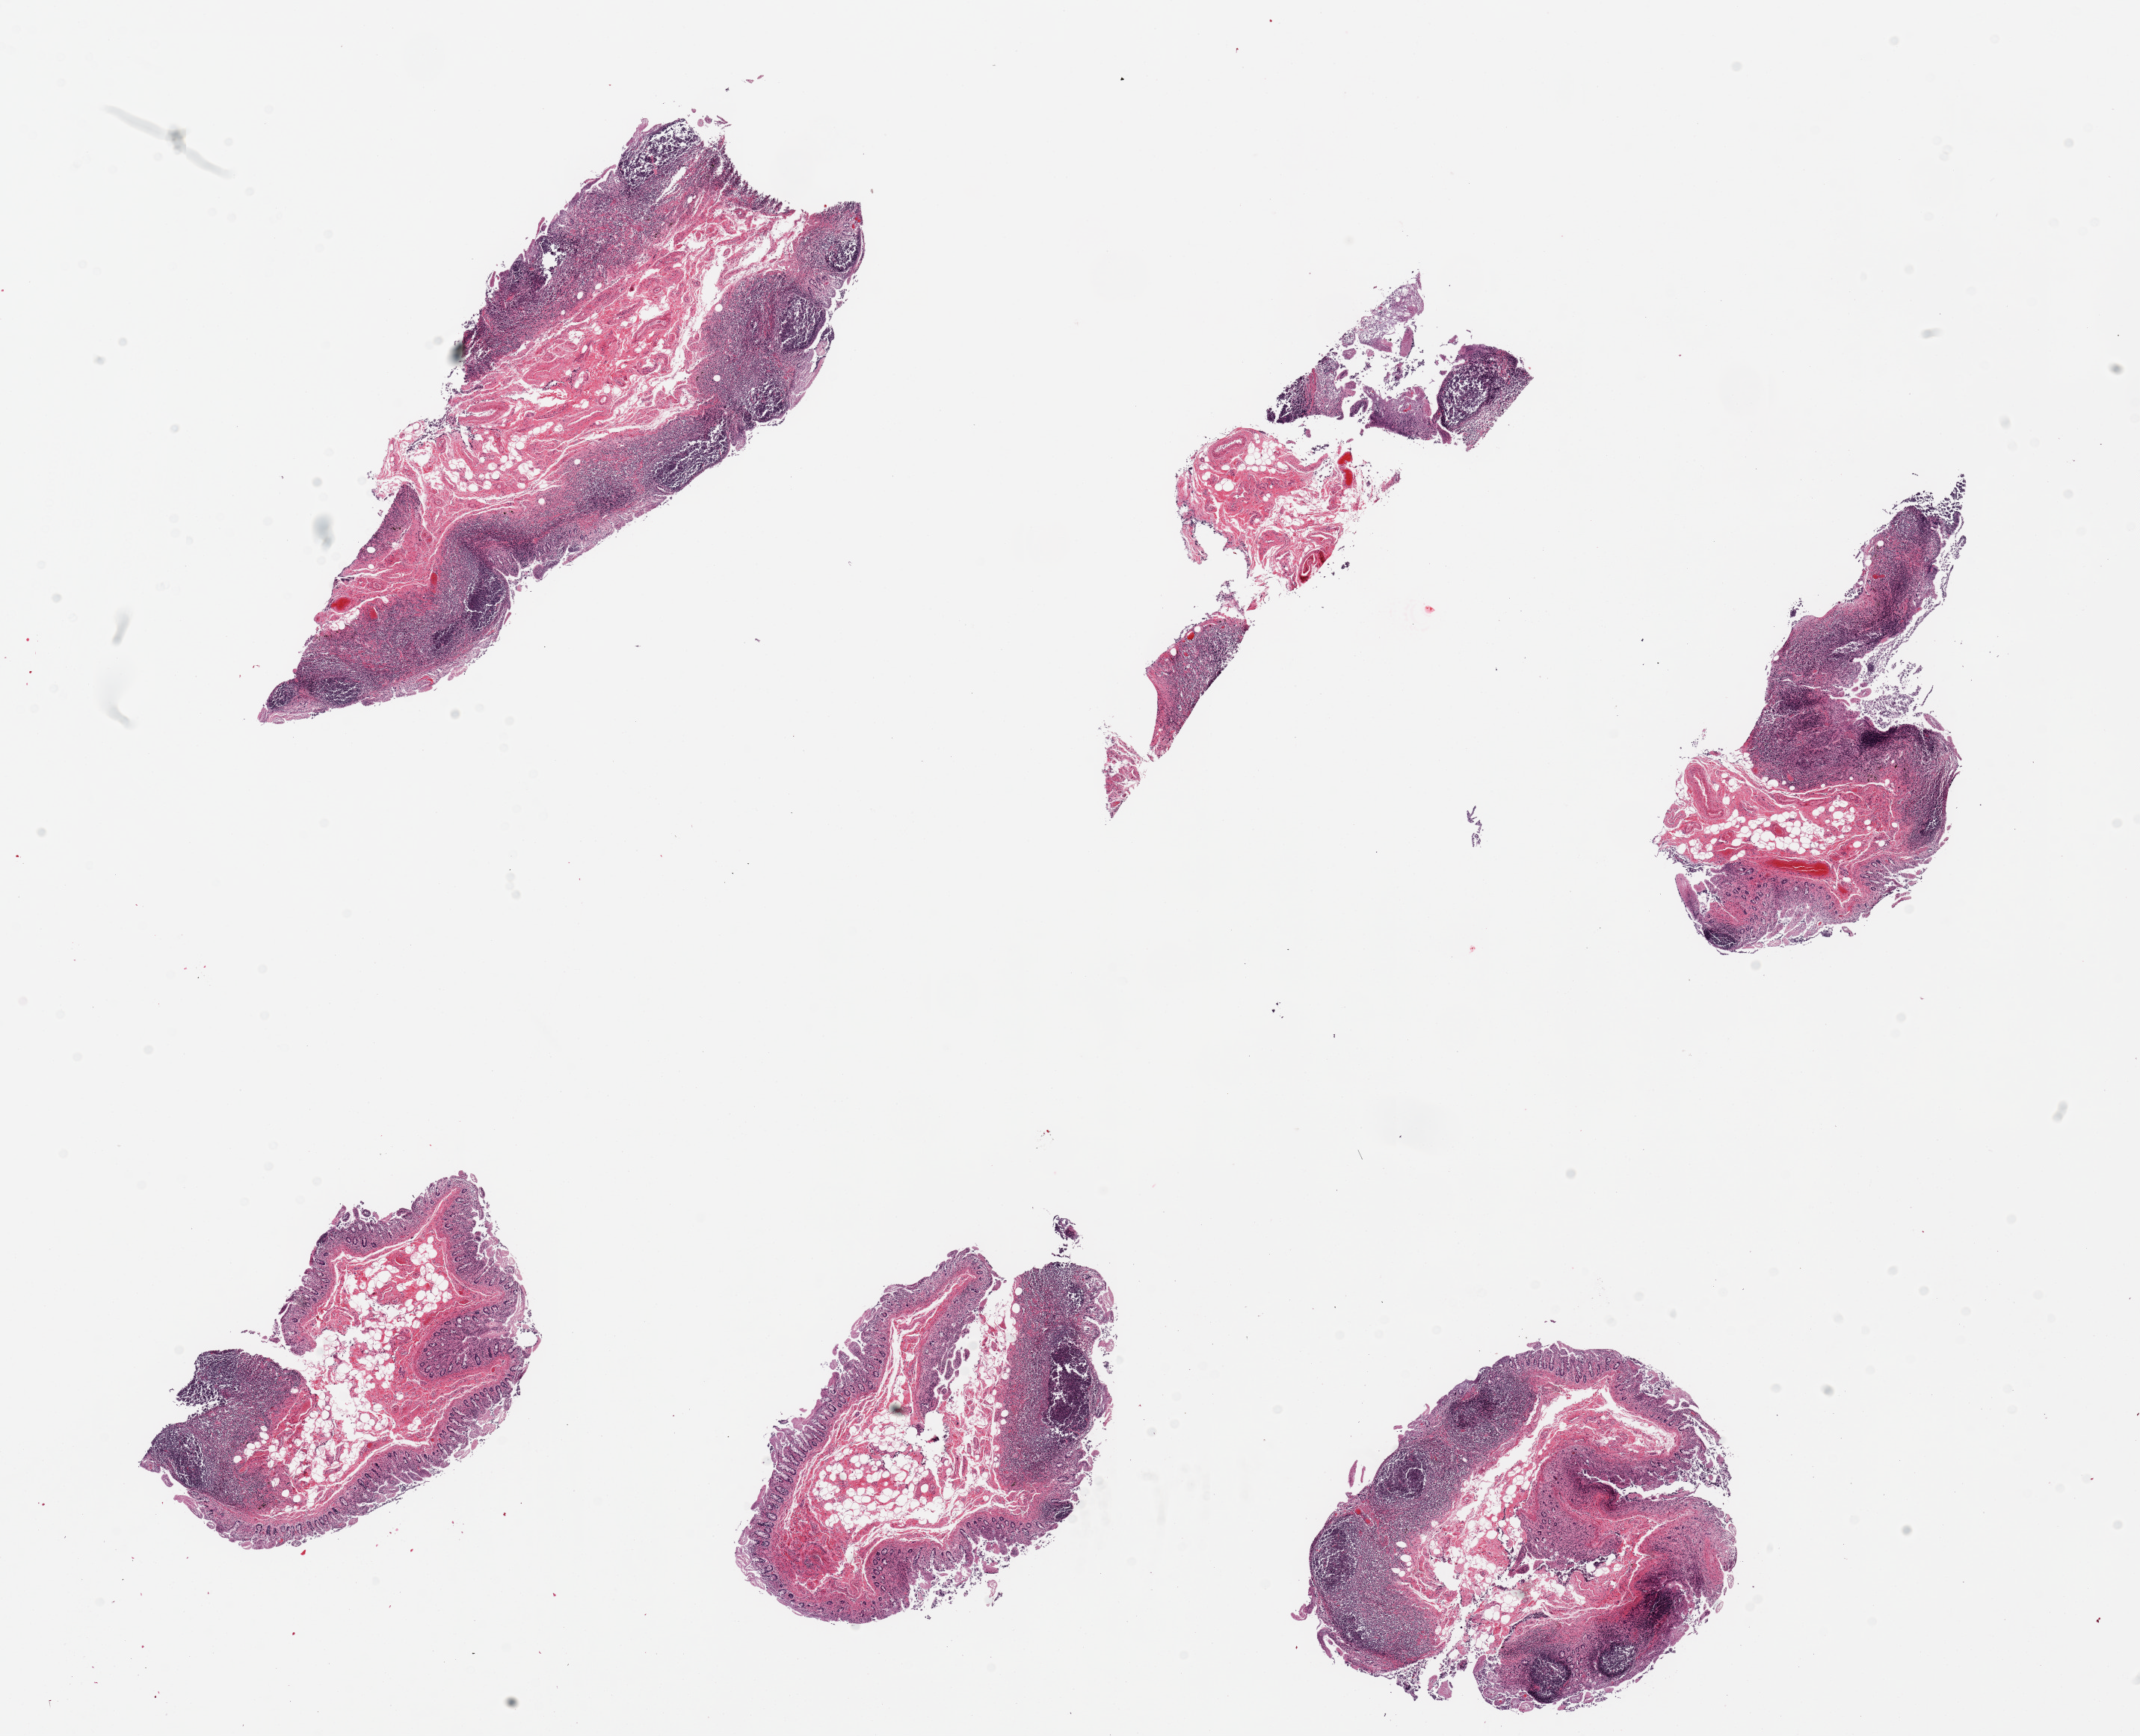
H&E whole-slide image — whole scanned area (about 22.6 x 18.4 mm) shown as a low-resolution overview, PAXgene-fixed paraffin-embedded (PFPE) section, sampled site (target tissue): ileum, tissue donor sample. Male donor.
Reviewer comment on this tissue sample: 6 pieces; numerous lymphoid nodules.